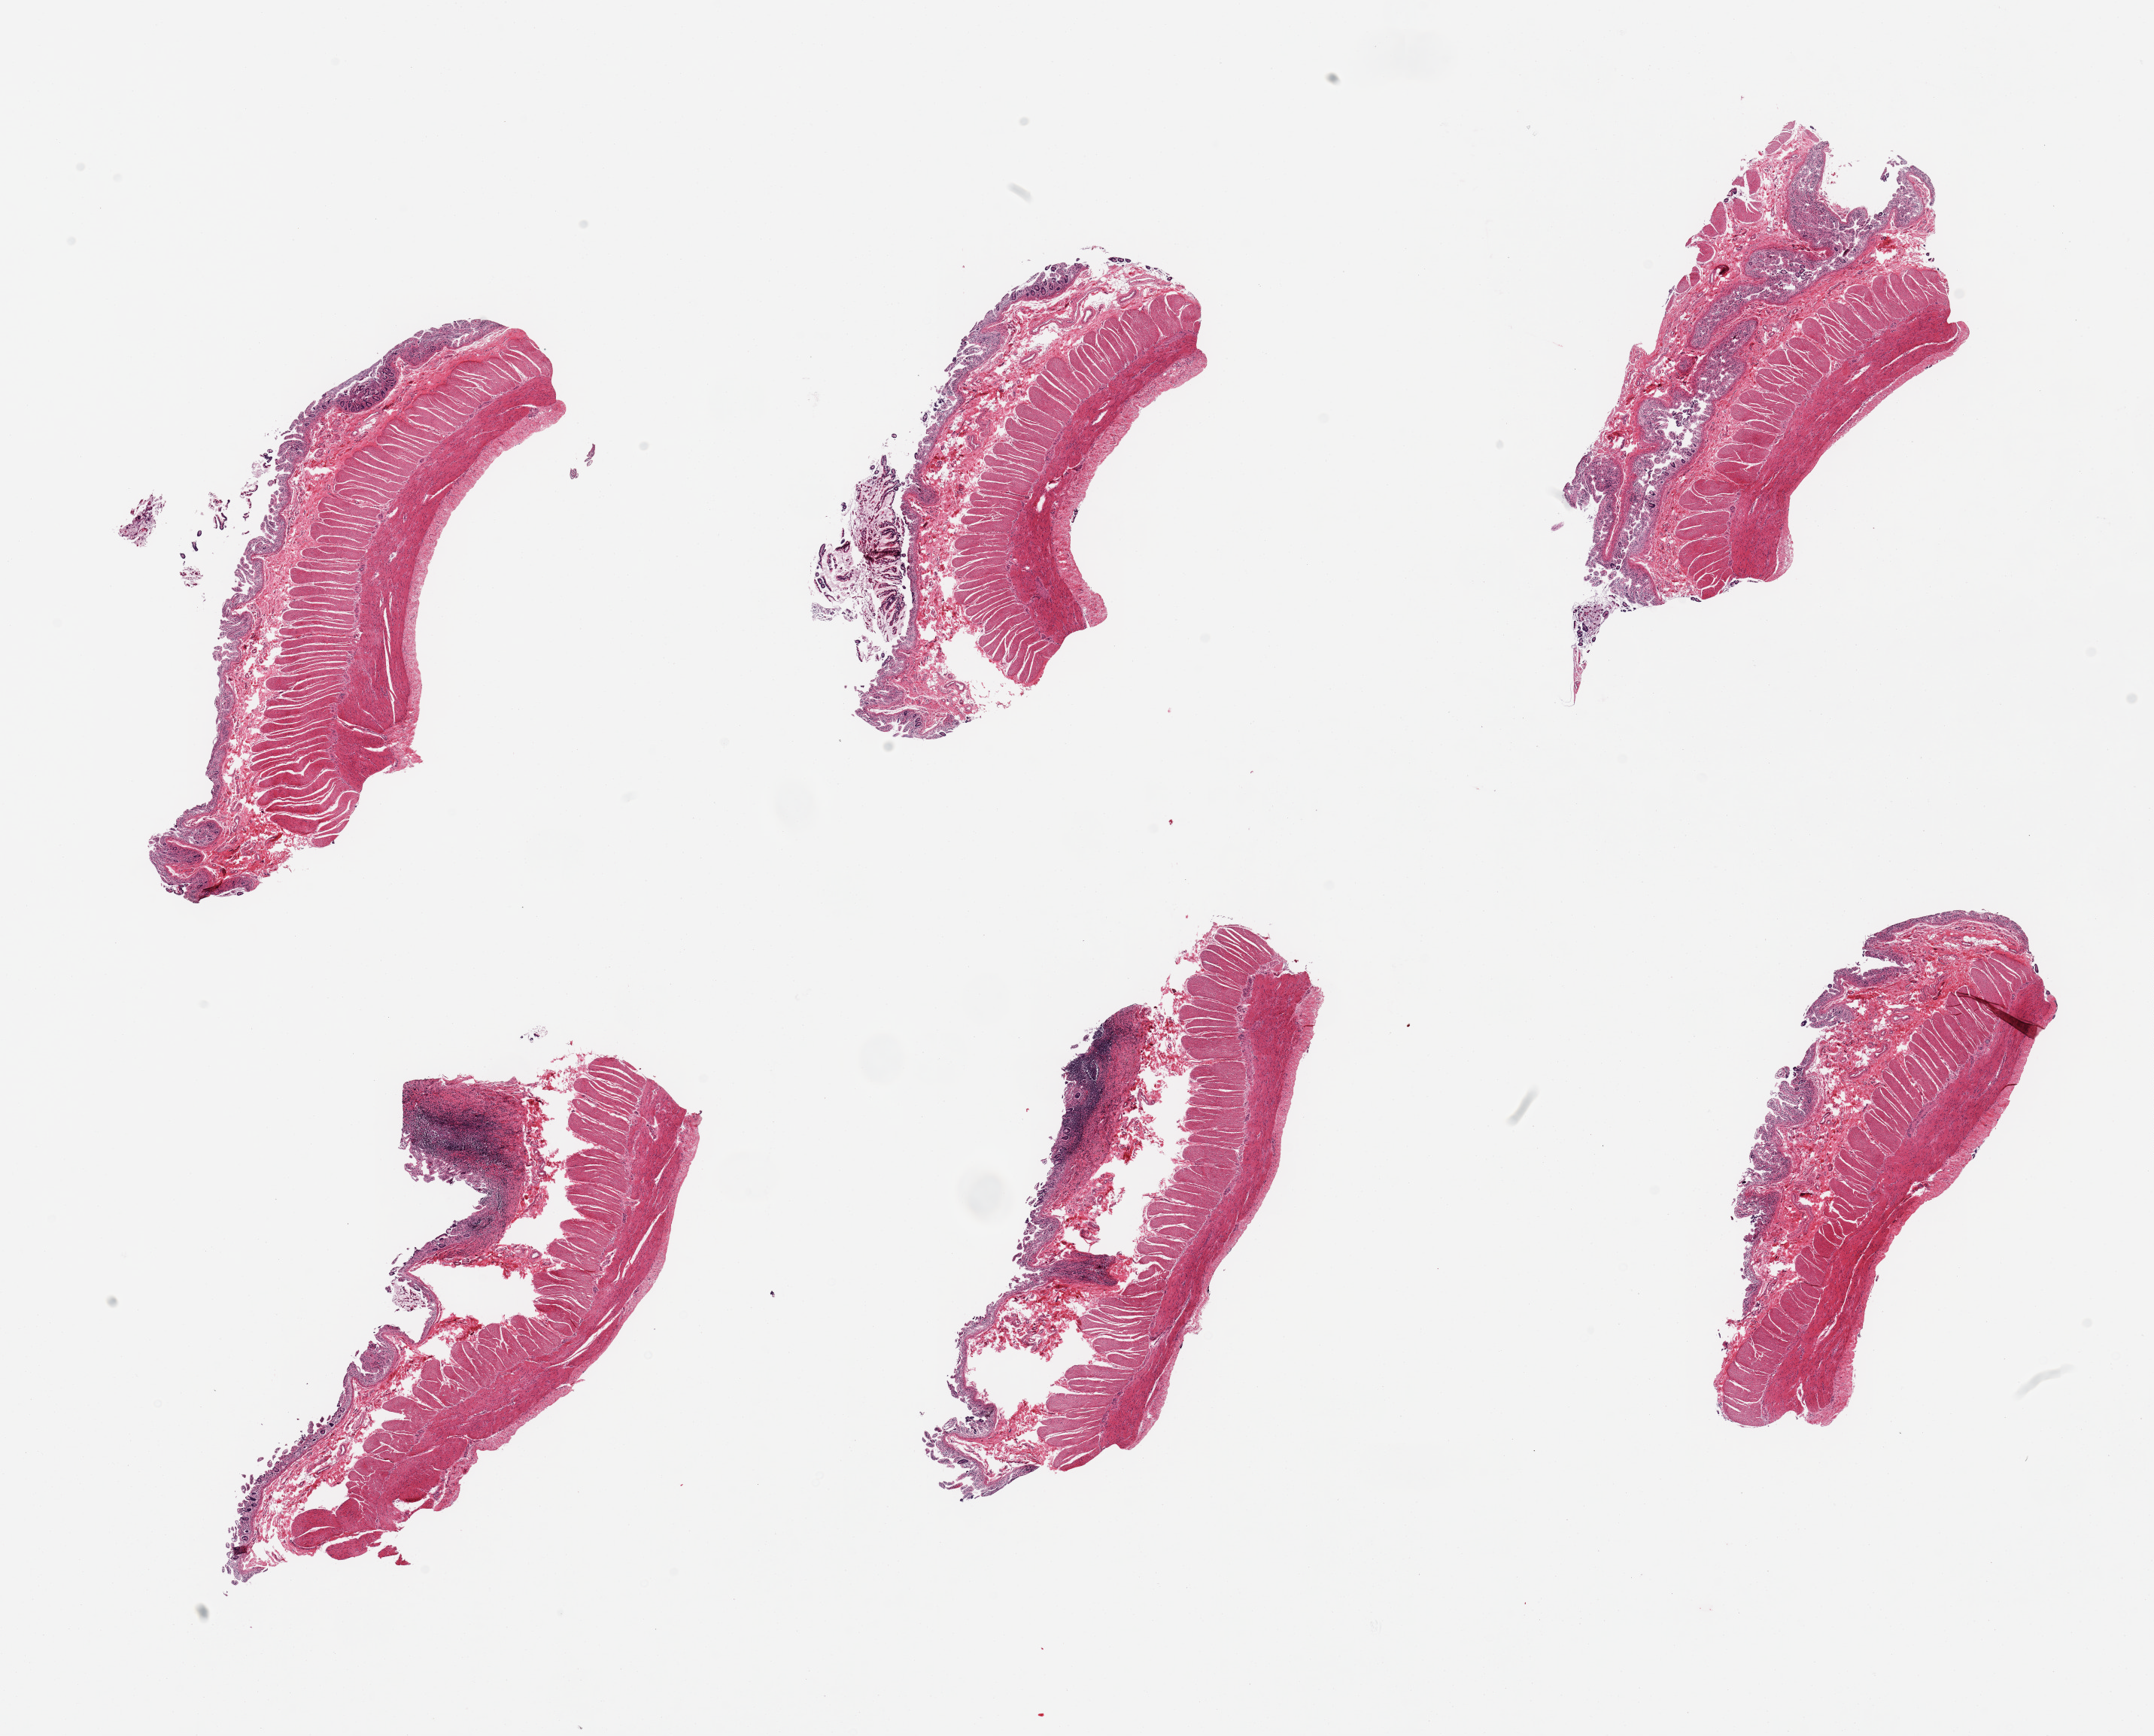
Haematoxylin and eosin whole-slide image, brightfield — a low-resolution overview of the entire scanned area, about 22.6 x 18.3 mm (acquisition: 20x scan); PAXgene-fixed paraffin-embedded (PFPE) section; section of ileum (target tissue); donor tissue sample. Female donor.
Reviewer comment on this tissue sample: 6 pieces; full thickness sections with largely autolyzed mucosa and only focal lymphoid tissue (target).